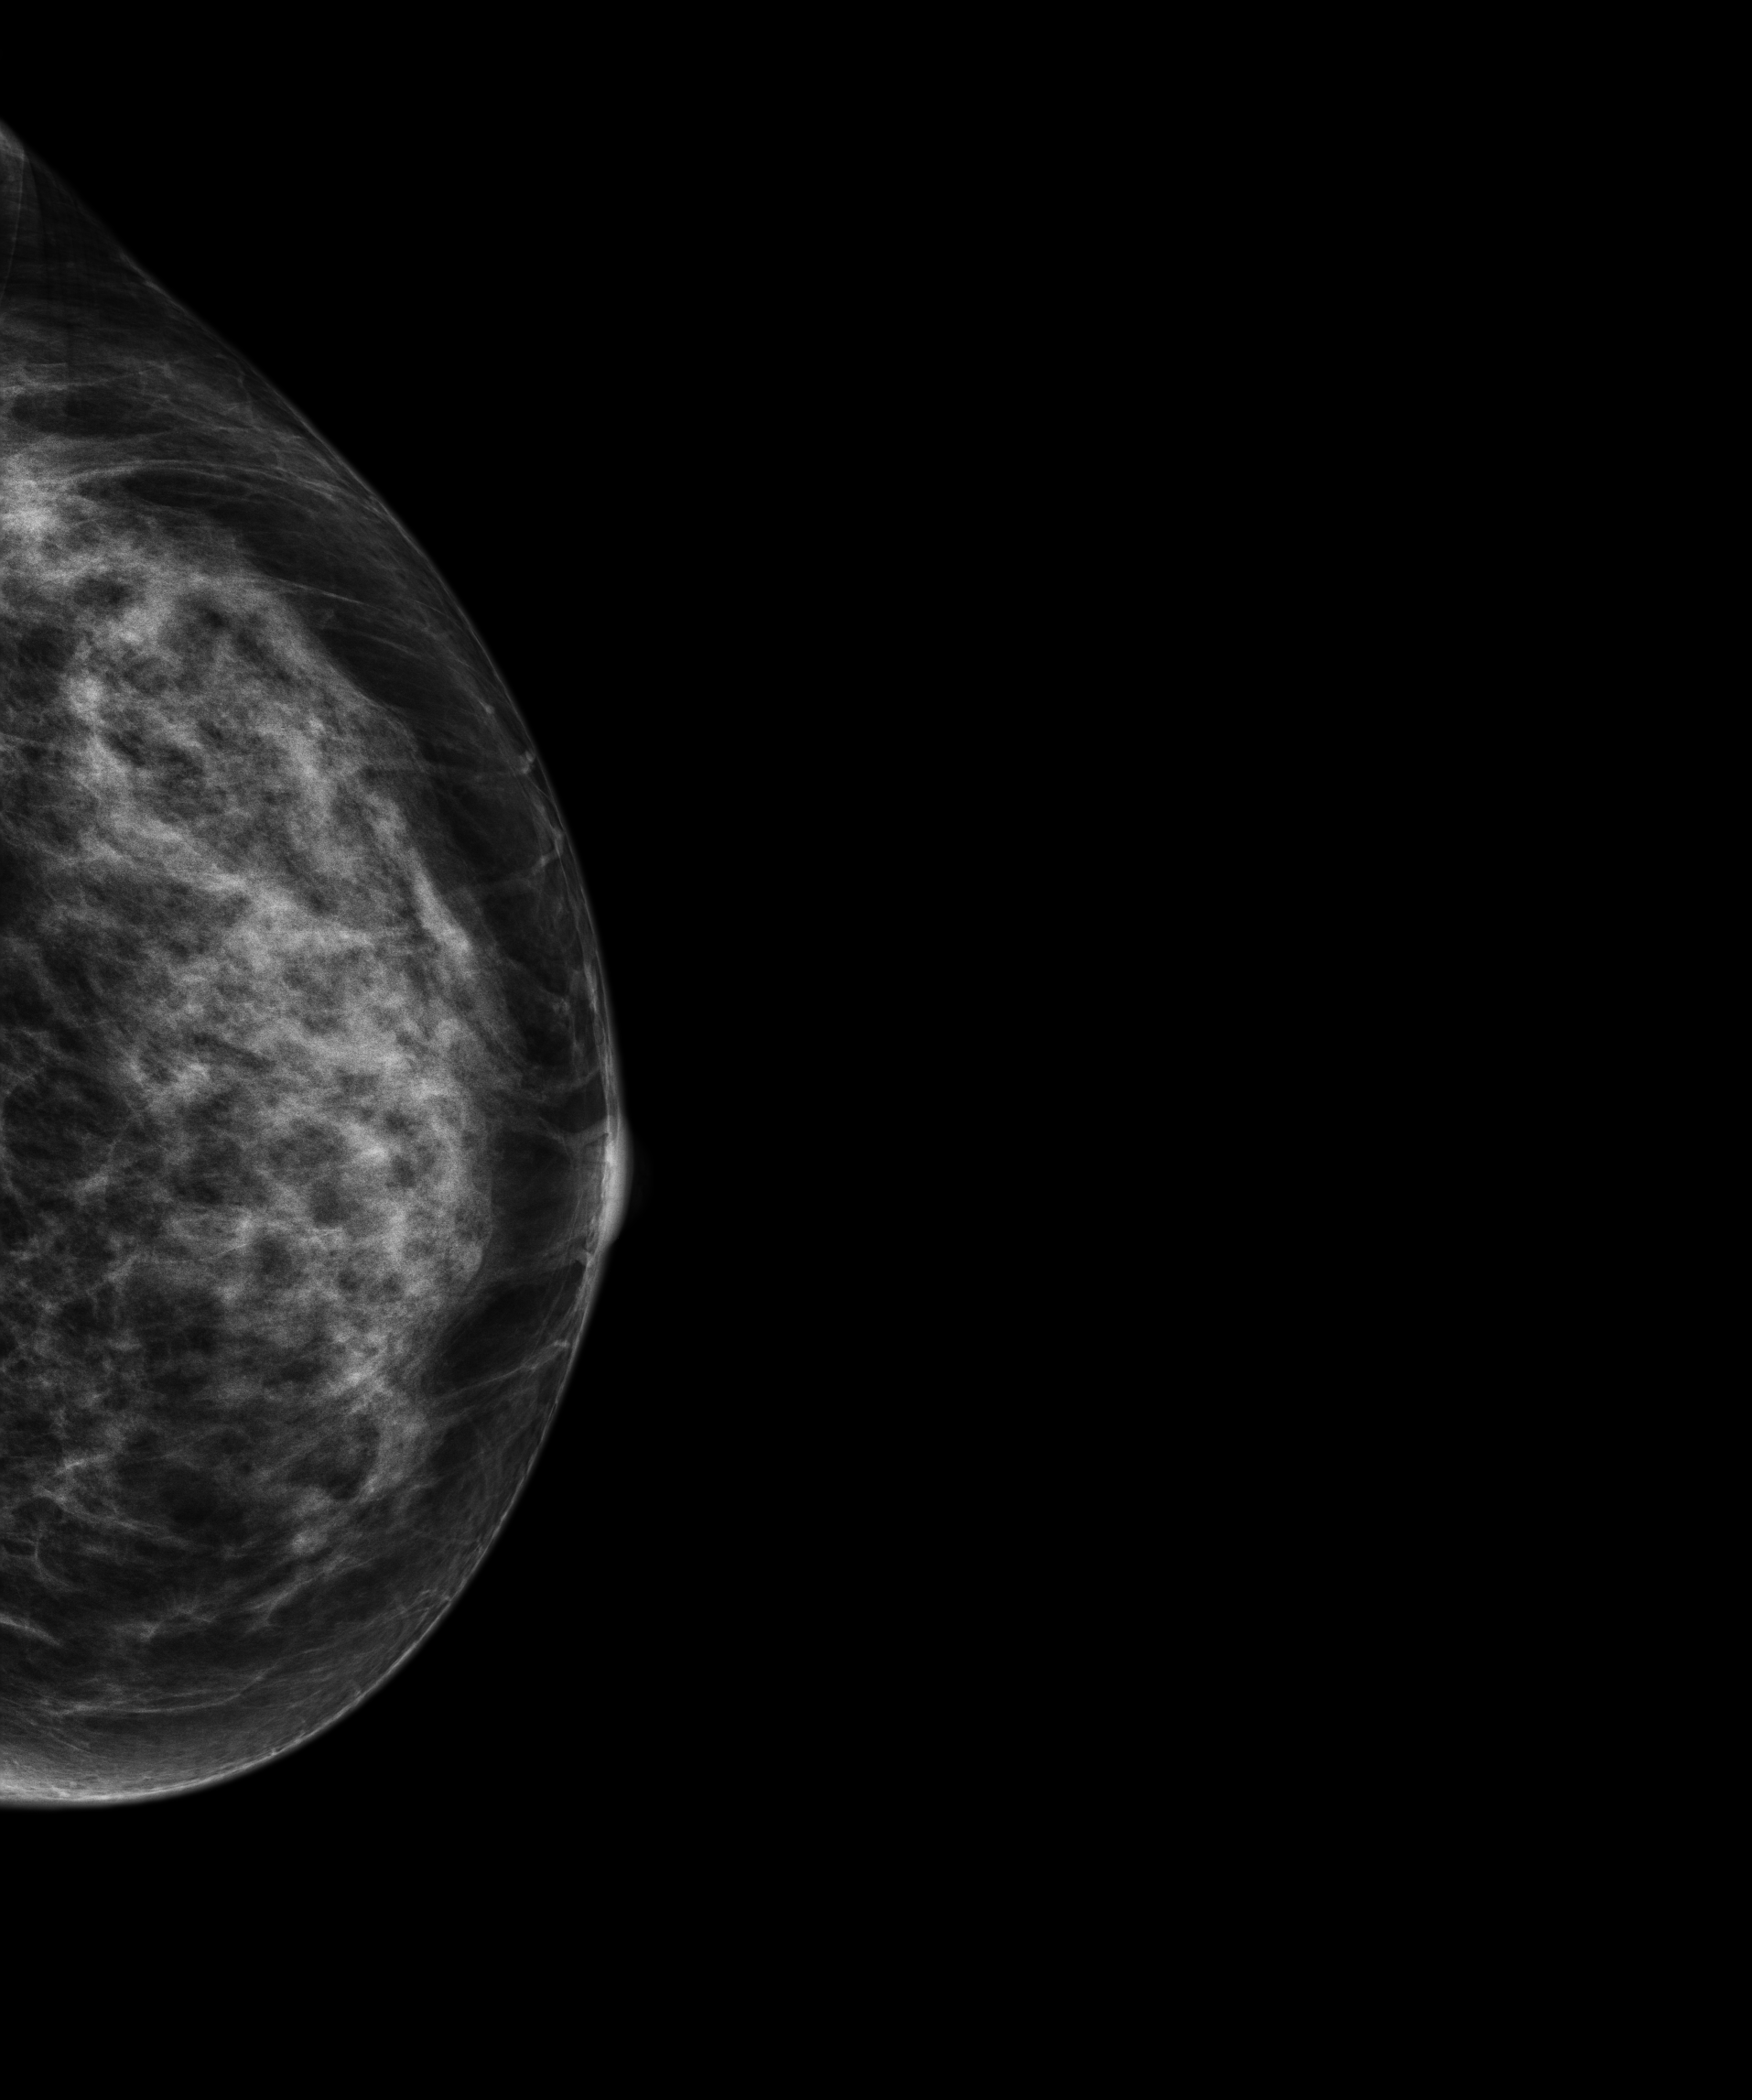
Full-field digital mammogram (FFDM), left breast, cranio-caudal projection, screening examination, compressed breast thickness 55 mm. Patient: female, 56 years.
Final BI-RADS assessment for this screening round (tomosynthesis exam, both breasts): category 1.